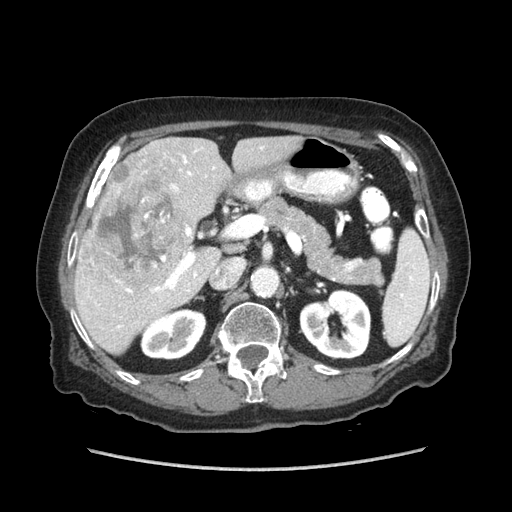
Contrast-enhanced abdominal CT (liver protocol), one axial slice. Slice 41 of 89 in the series (ordered by position). Reconstruction kernel STANDARD. Soft-tissue window (W 400 / L 40 HU). 2.5 mm slice thickness. 512 × 512 image matrix, field of view 360 × 360 mm. From the clinical record (not read from this slice): diagnosis: hepatocellular carcinoma (patient treated with transarterial chemoembolisation; whether this scan precedes or follows treatment is not stated here); TNM stage (as recorded): Stage-IIIA; Child-Pugh class: A; tumour differentiation: well differentiated; tumour nodularity: multinodular.
Structures marked on this image (semi-automatic segmentation, software-assisted and operator-edited):
- liver parenchyma outside the tumour (the mass and vessels are separate outlines, so this box may not span the whole liver): bounding box (x1, y1, x2, y2) in pixels: (74, 136, 302, 354)
- mass: (91, 162, 189, 285)
- liver vessels: (117, 147, 263, 328)